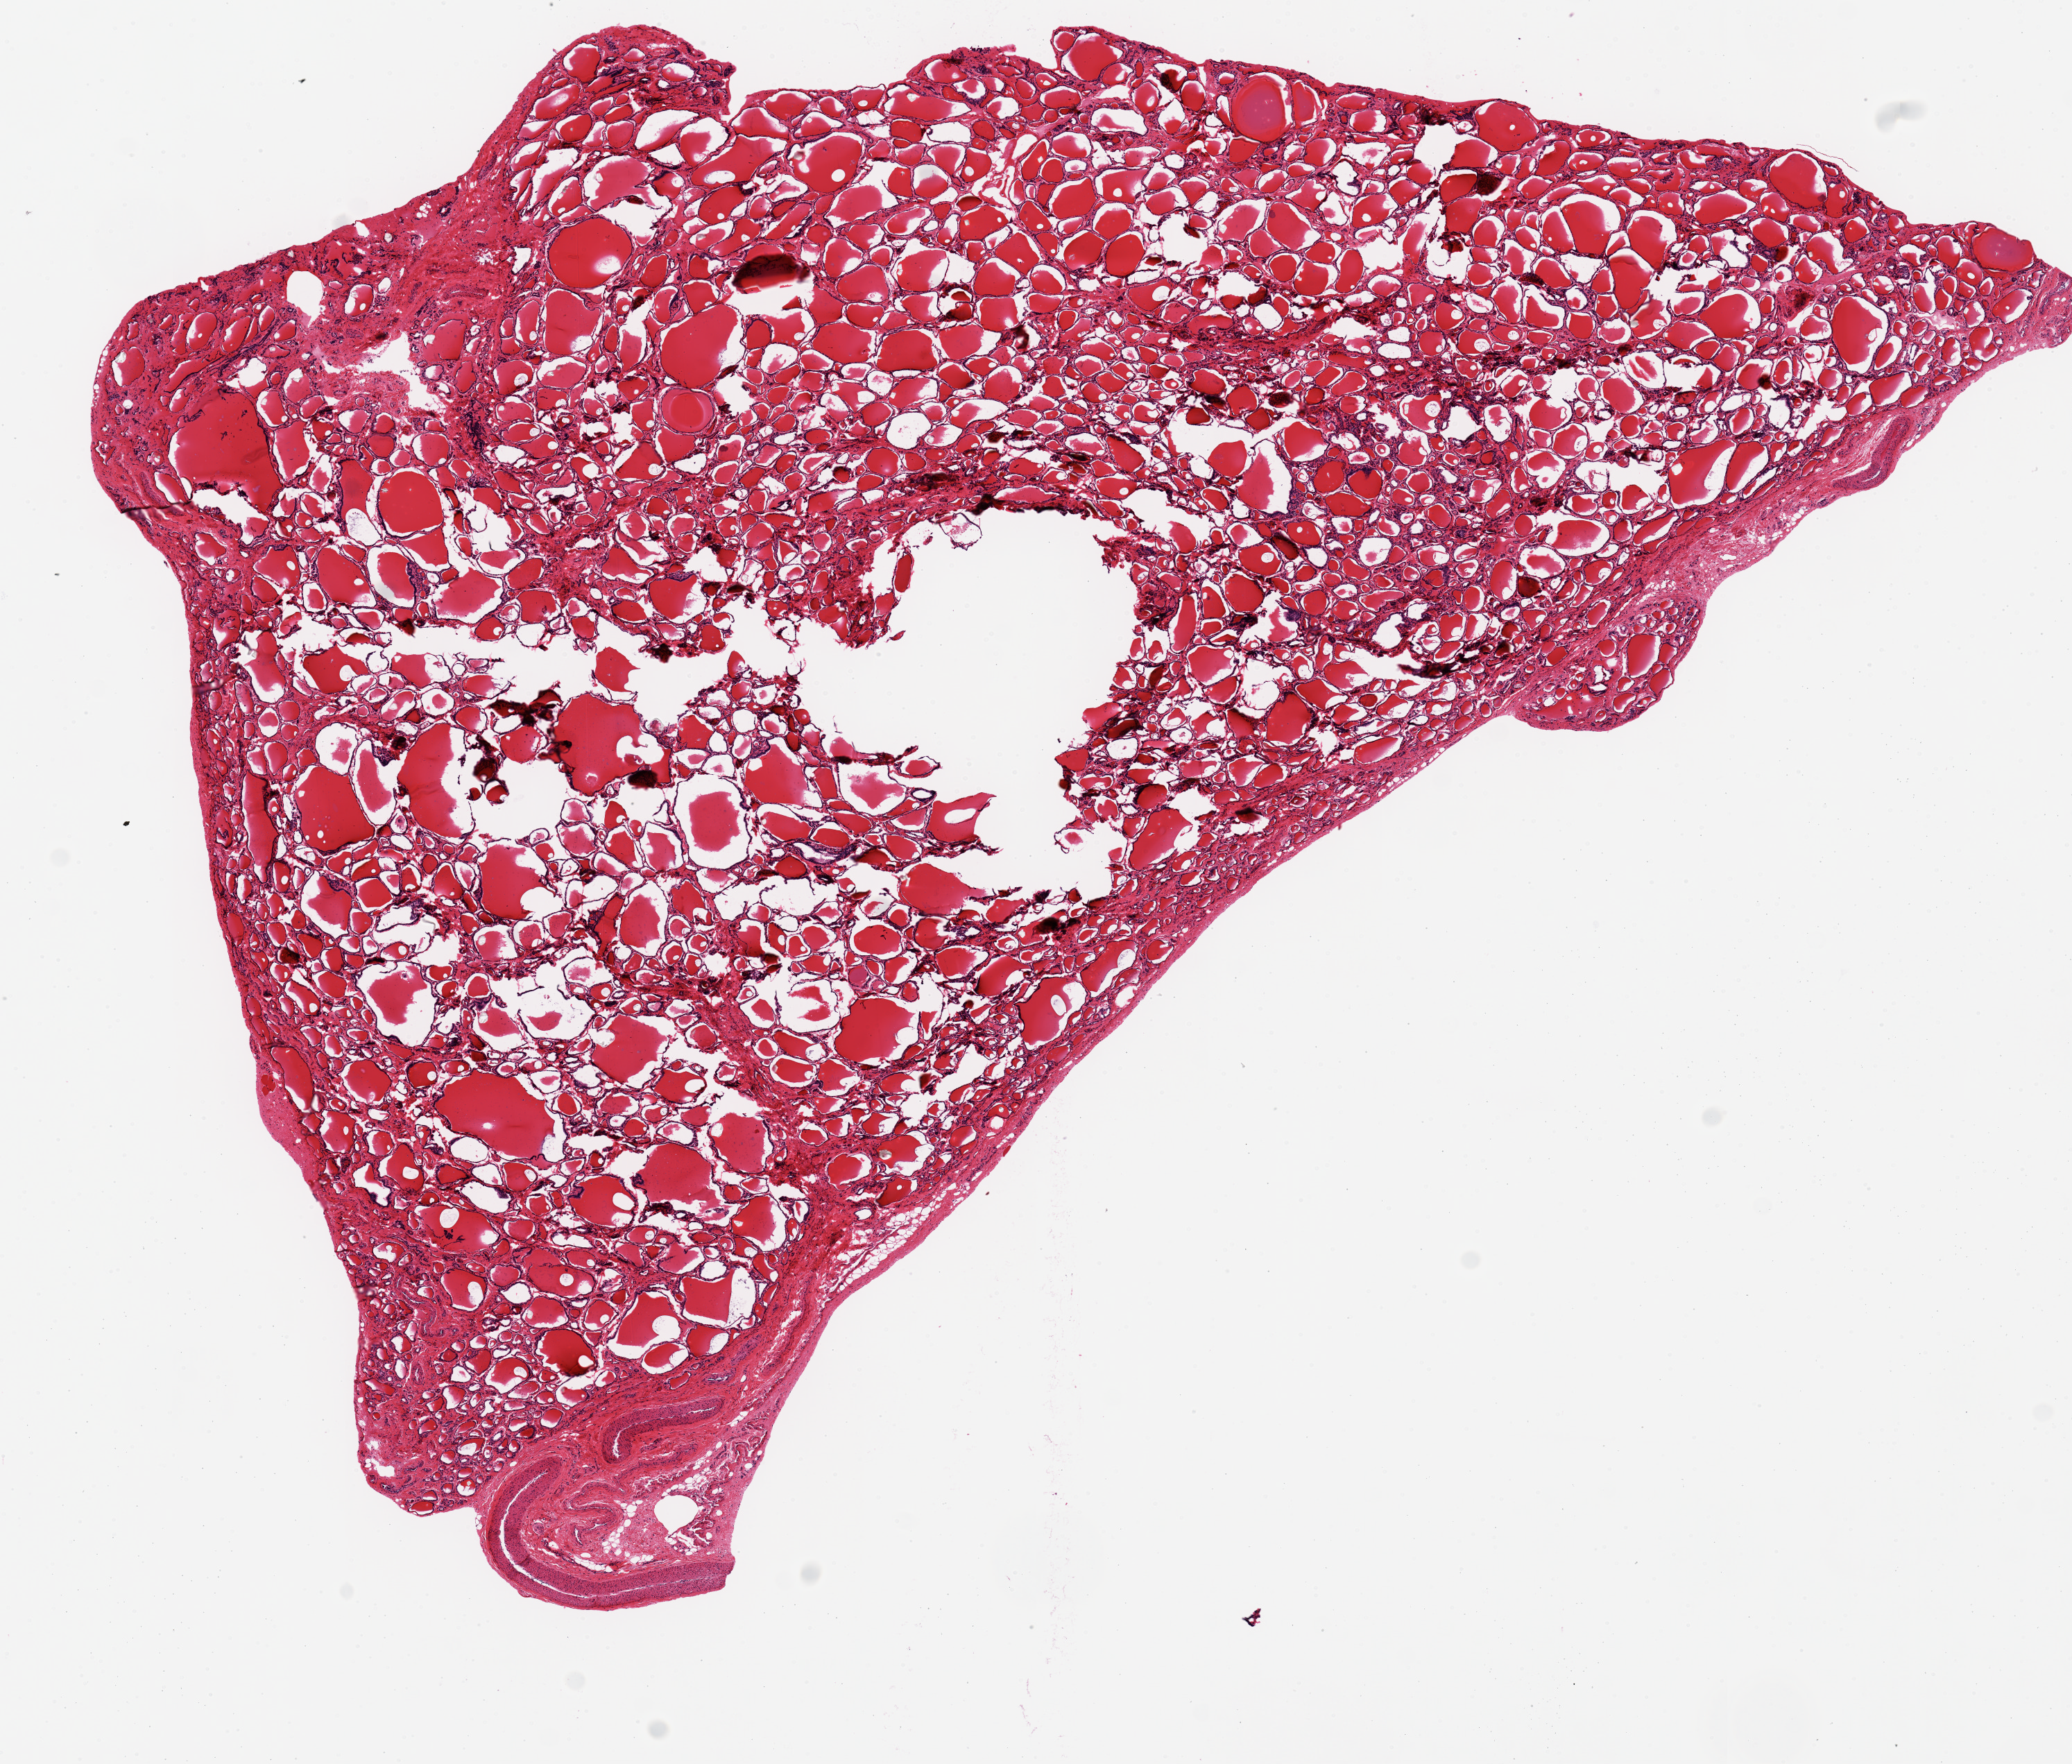
Whole-slide image, haematoxylin and eosin stain — a low-resolution overview of the entire scanned area, about 11.8 x 10.1 mm, PAXgene-fixed, paraffin-embedded tissue, target tissue: thyroid, donor tissue sample. Male donor.
* review note (as recorded): OK for analysis